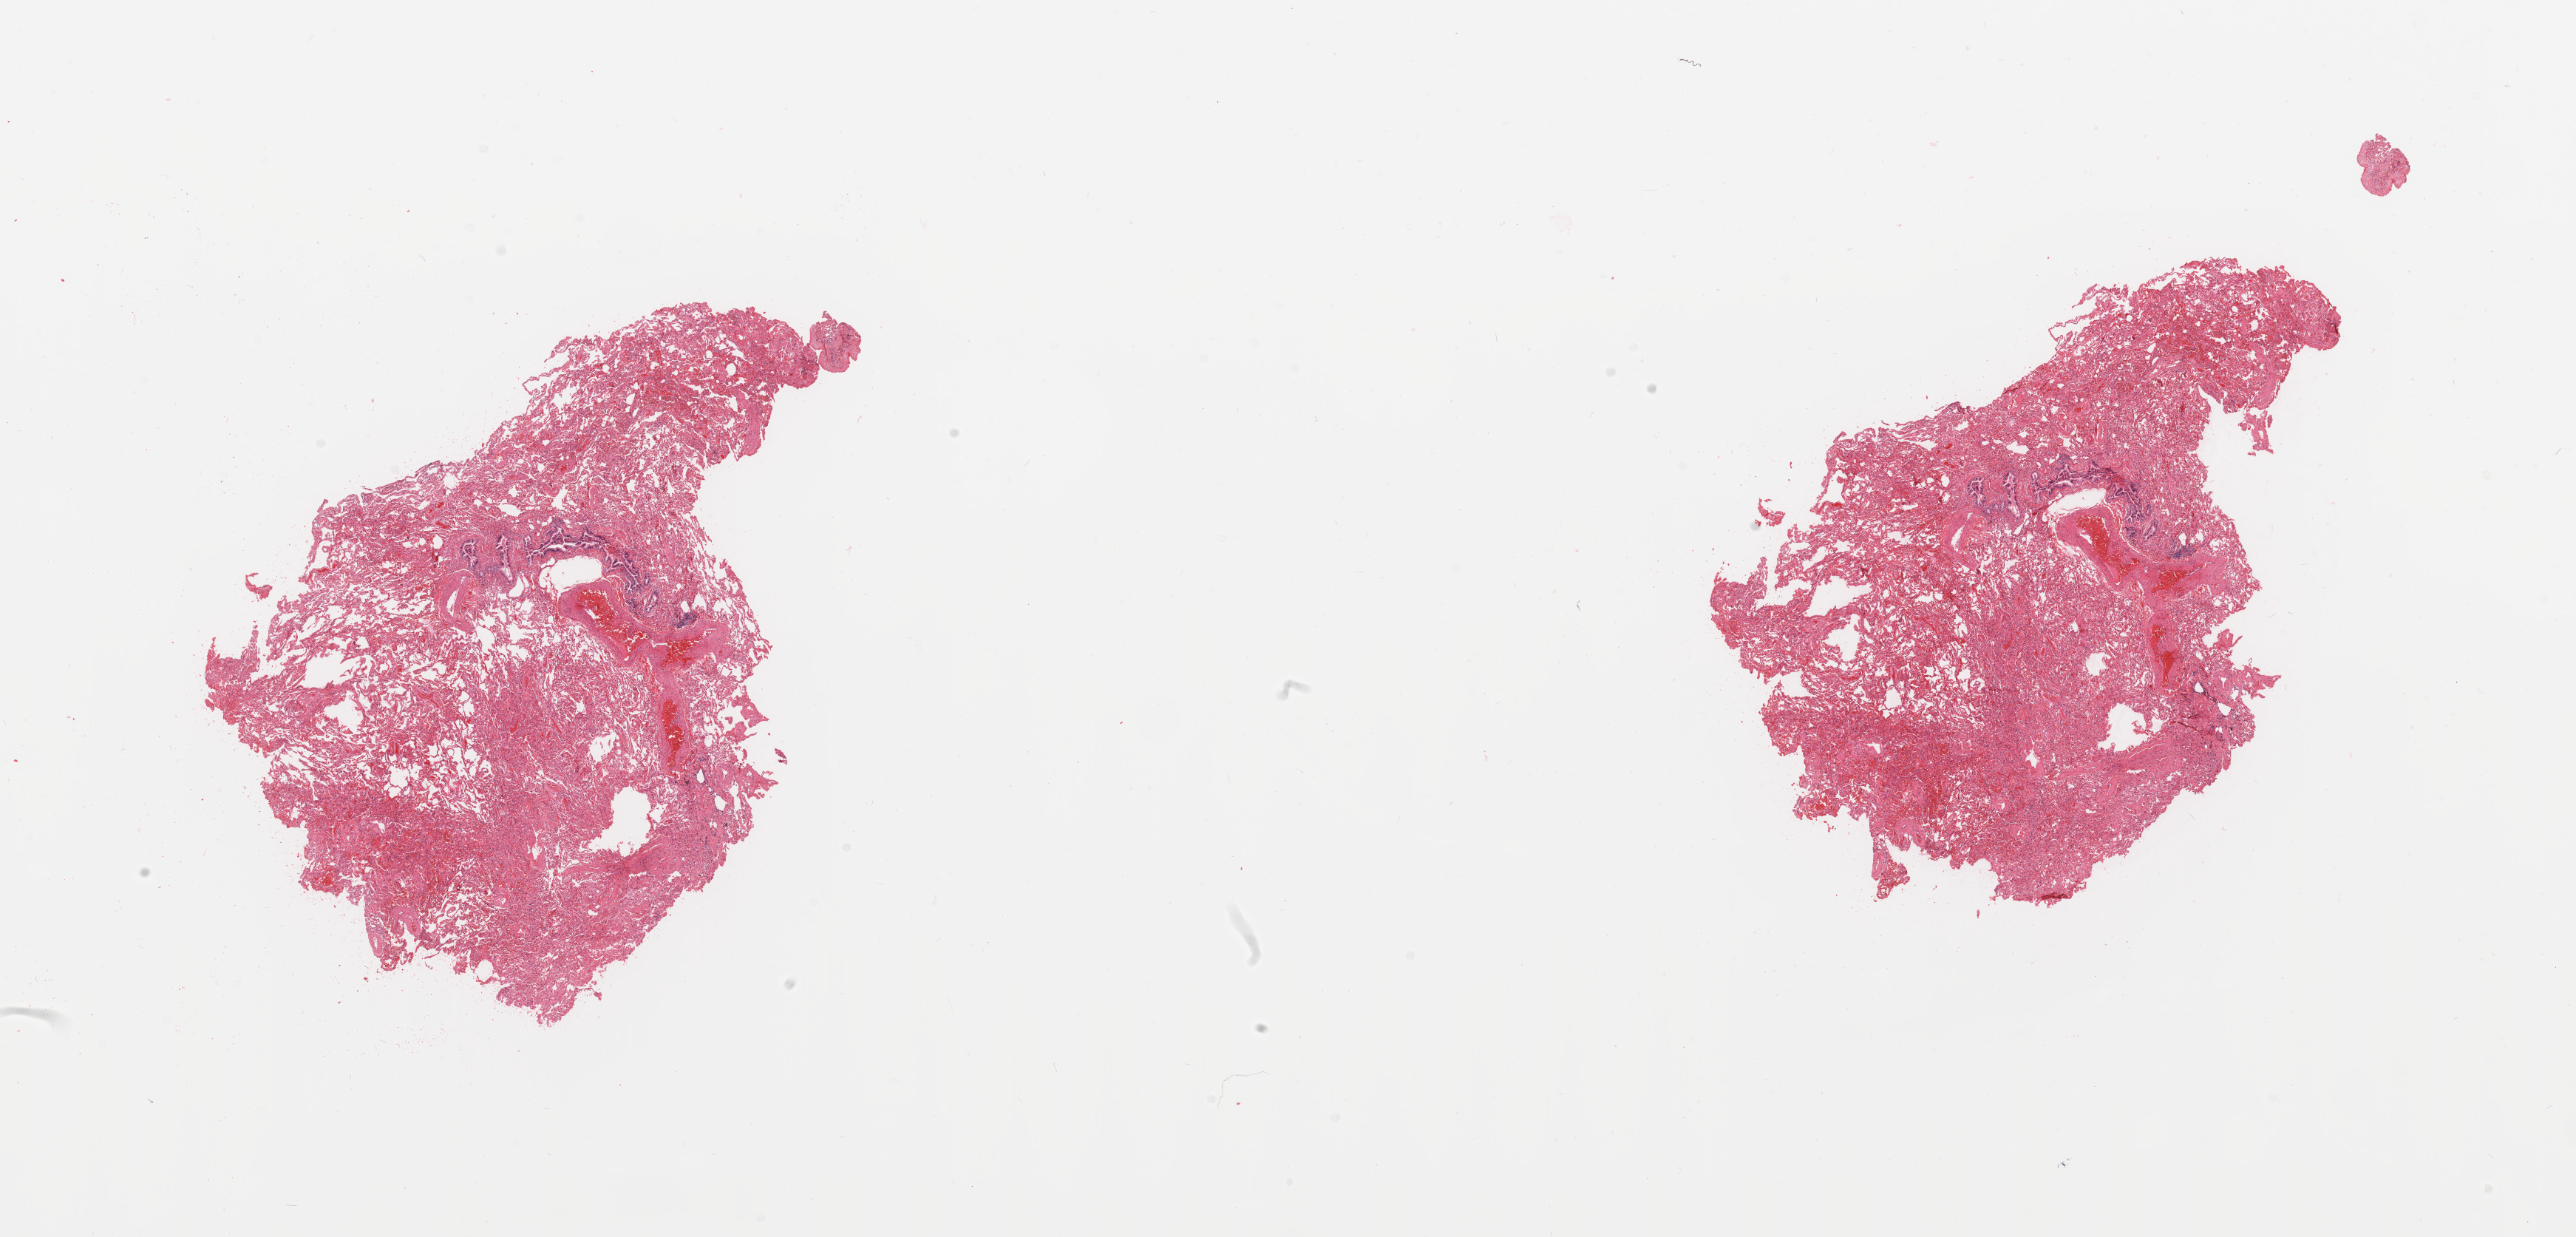
Whole-slide histology image, H&E-stained, shown as a low-resolution overview of the whole scanned area (about 27.6 x 13.2 mm, from a 20x scan); normal (non-tumour) tissue sample, sampled site: lung. Patient: female, age 64 years.
• this section: normal (non-tumour) tissue from the same patient
• patient diagnosis: Squamous cell carcinoma, NOS